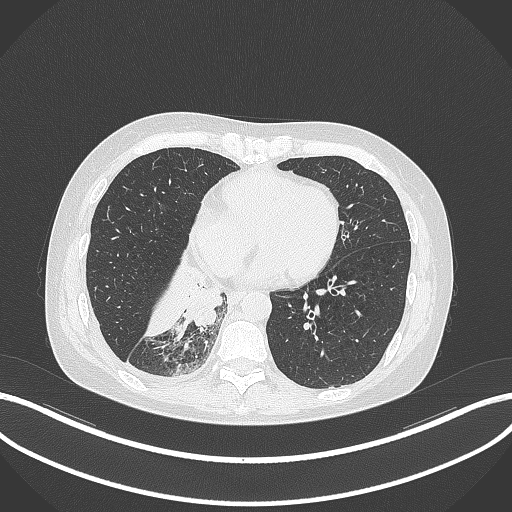
Chest CT, one axial slice; position 107 of 329 along the scan axis; reconstruction kernel B70f; 120 kVp; lung window (W 1500 / L -600 HU); 1 mm slice thickness; 512 × 512 image matrix, field of view 400 × 400 mm. Patient: female, 63 years. From the clinical record (not read from this slice): clinical TNM (as recorded): T1c N0 M0.
Structures marked on this image (rectangle marked by the reading radiologist):
- lung tumour (recorded histology: adenocarcinoma): bounding box <178,276,229,329> (left, top, right, bottom; pixels)